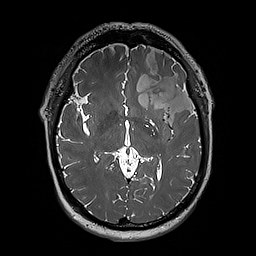
Brain MRI from a brain-tumour surgery series, one axial slice. Position 115 of 192 along the scan axis. 1 mm slice thickness. 256 × 256 image matrix. From the clinical record (not read from this slice): histopathology: Oligodendroglioma; WHO grade: 3; IDH mutation: yes; tumour location: Left Sylvian Fissure (Temporal).
Annotated regions visible in this slice (expert manual segmentation):
- tumour: bounding box [x1, y1, x2, y2] px = [124, 49, 197, 124]